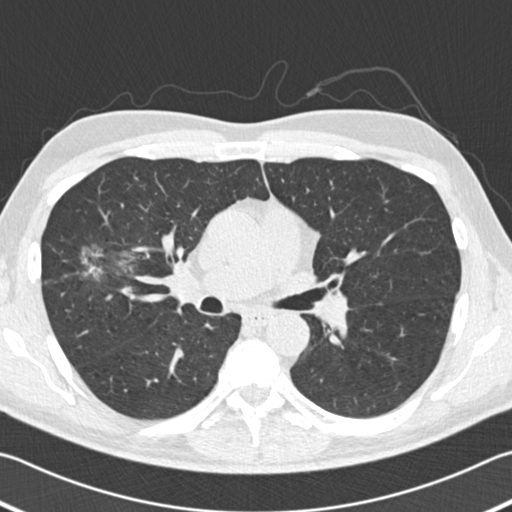
Low-dose screening chest CT, one axial slice. Reconstruction kernel B30f. Lung window (W 1500 / L -600 HU). 2 mm slice thickness. 512 × 512 image matrix, field of view 344 × 344 mm.
Annotated regions visible in this slice (outlined manually by an expert reader):
- lesion 1 (tumor, upper lobe of right lung): bounding box <81,245,125,280> (left, top, right, bottom; pixels)